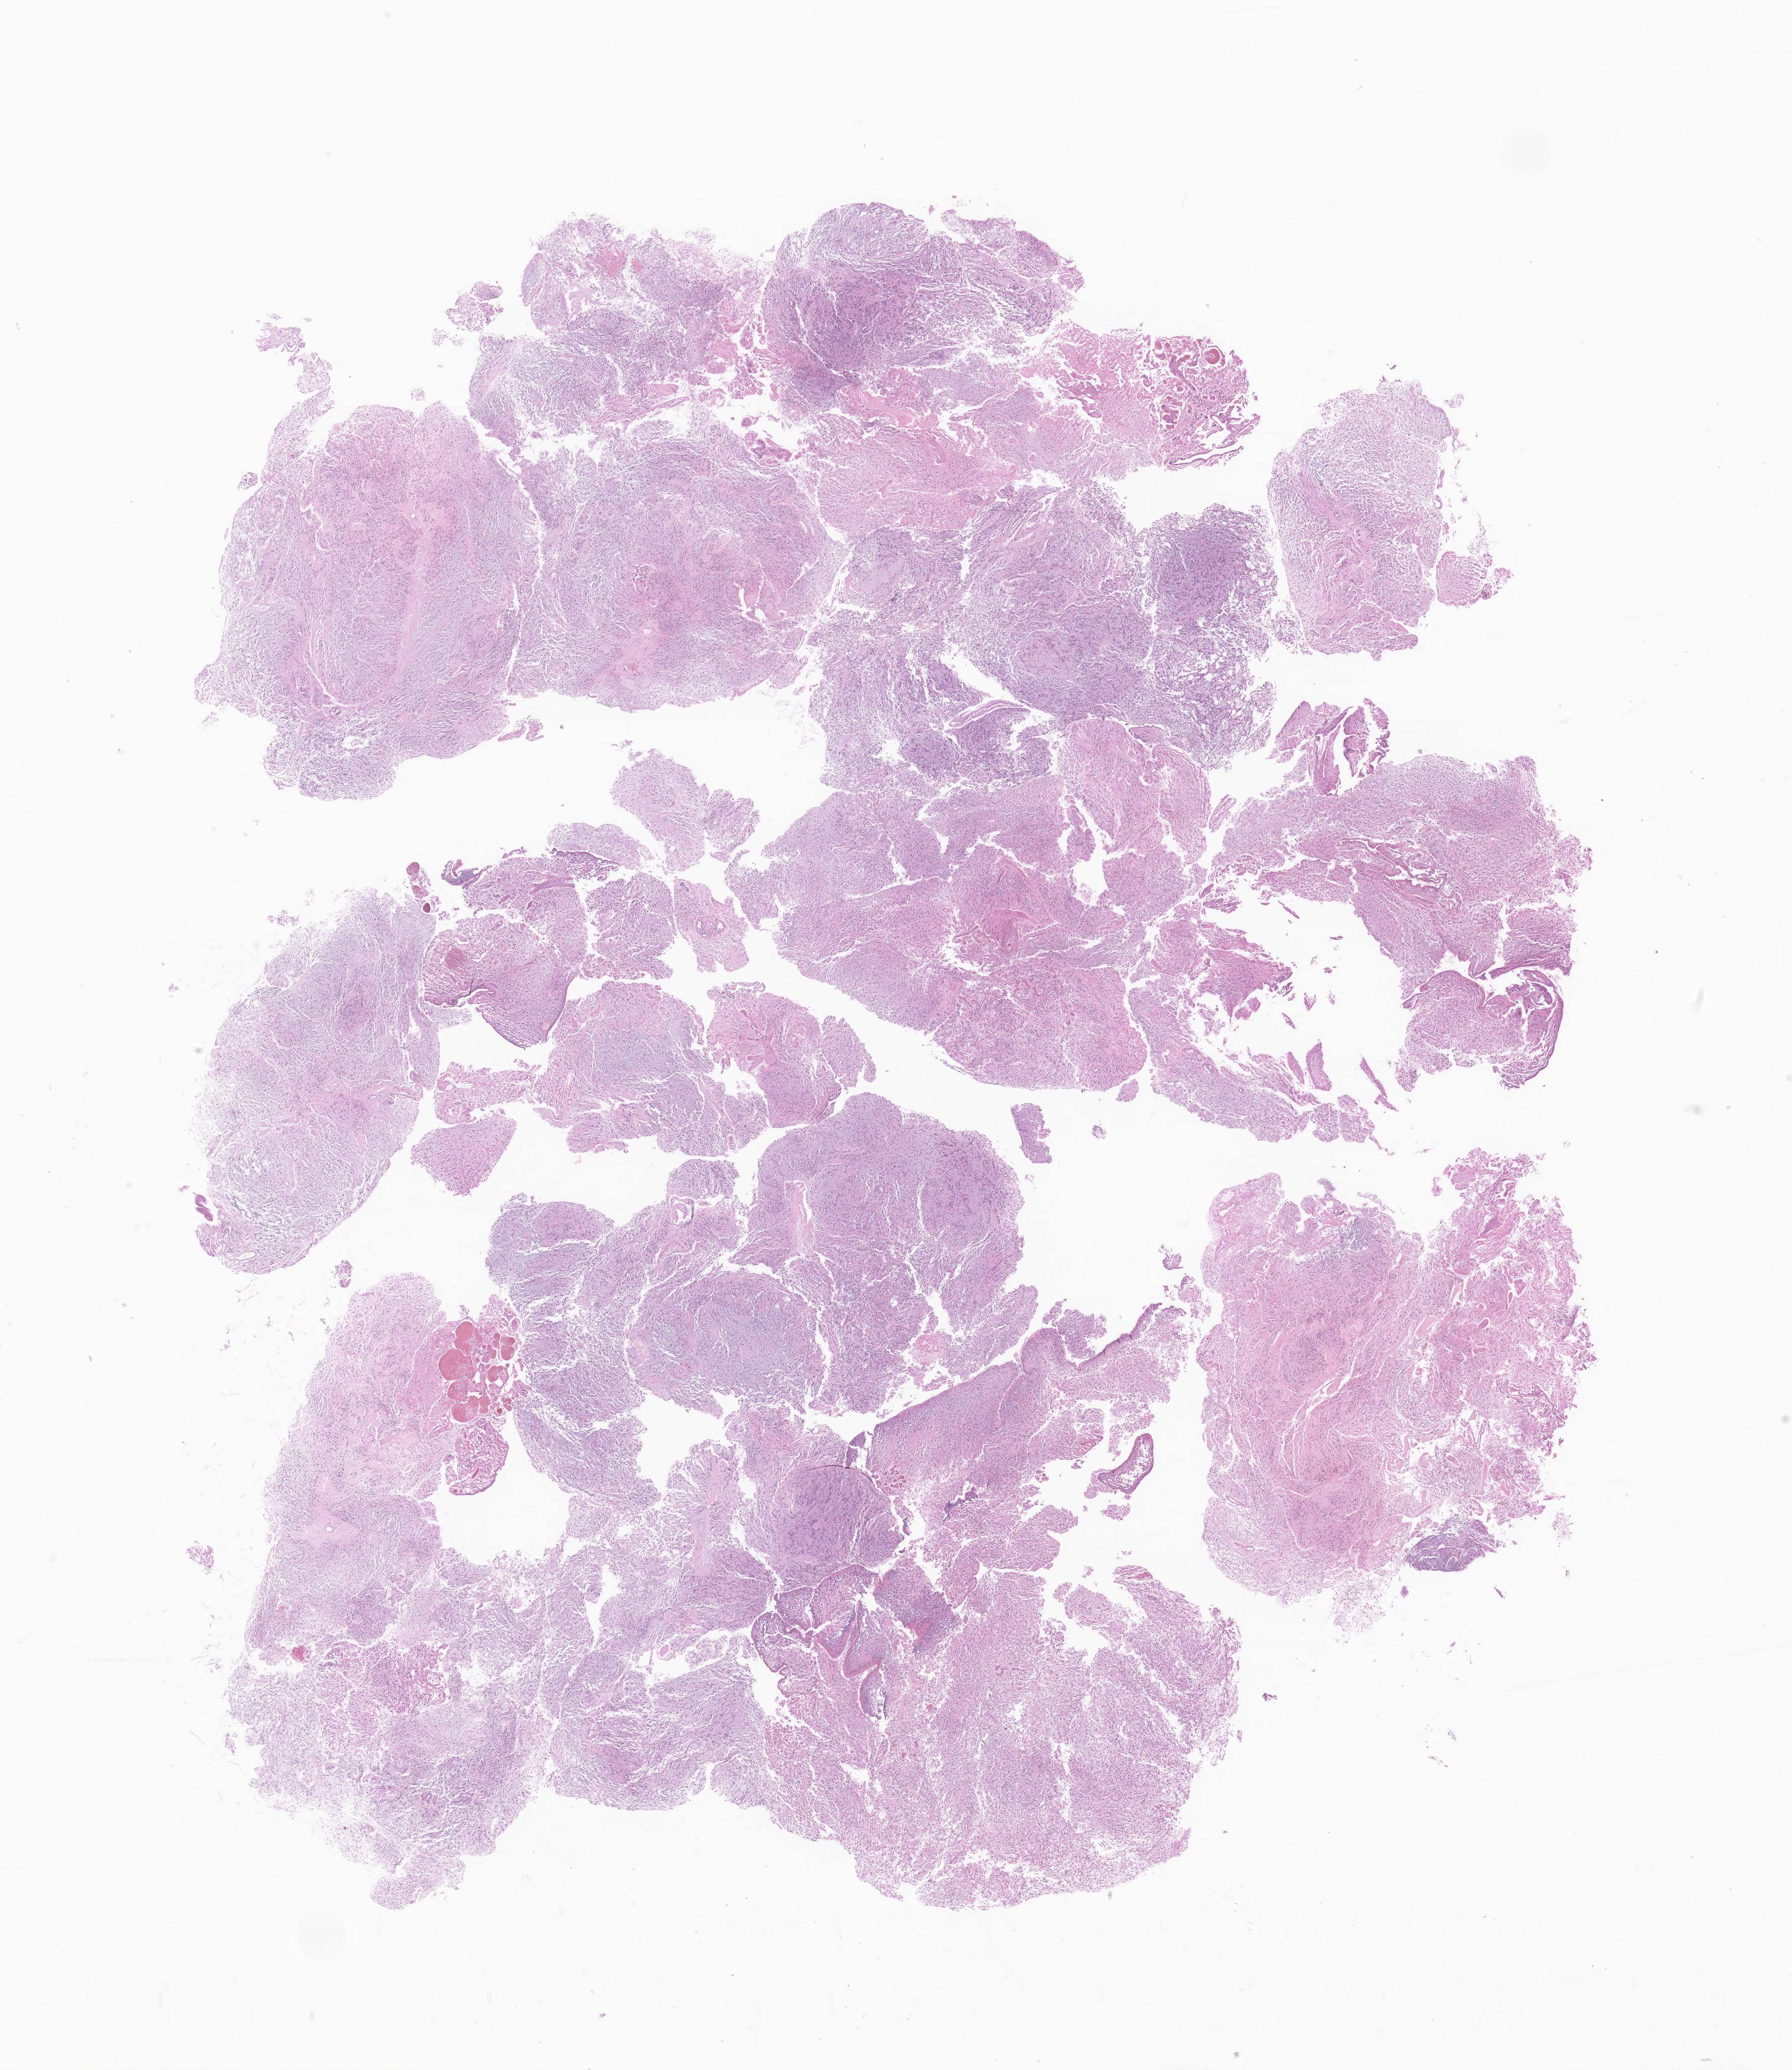
Whole-slide image, H&E stain of tumor tissue from the brain, low-resolution overview of the scanned area, about 18.4 x 21.2 mm; formalin-fixed, paraffin-embedded (FFPE) tissue. Patient: female, age 239 months.
Diagnosis (ICD-O-3 morphology term): Myxopapillary ependymoma.